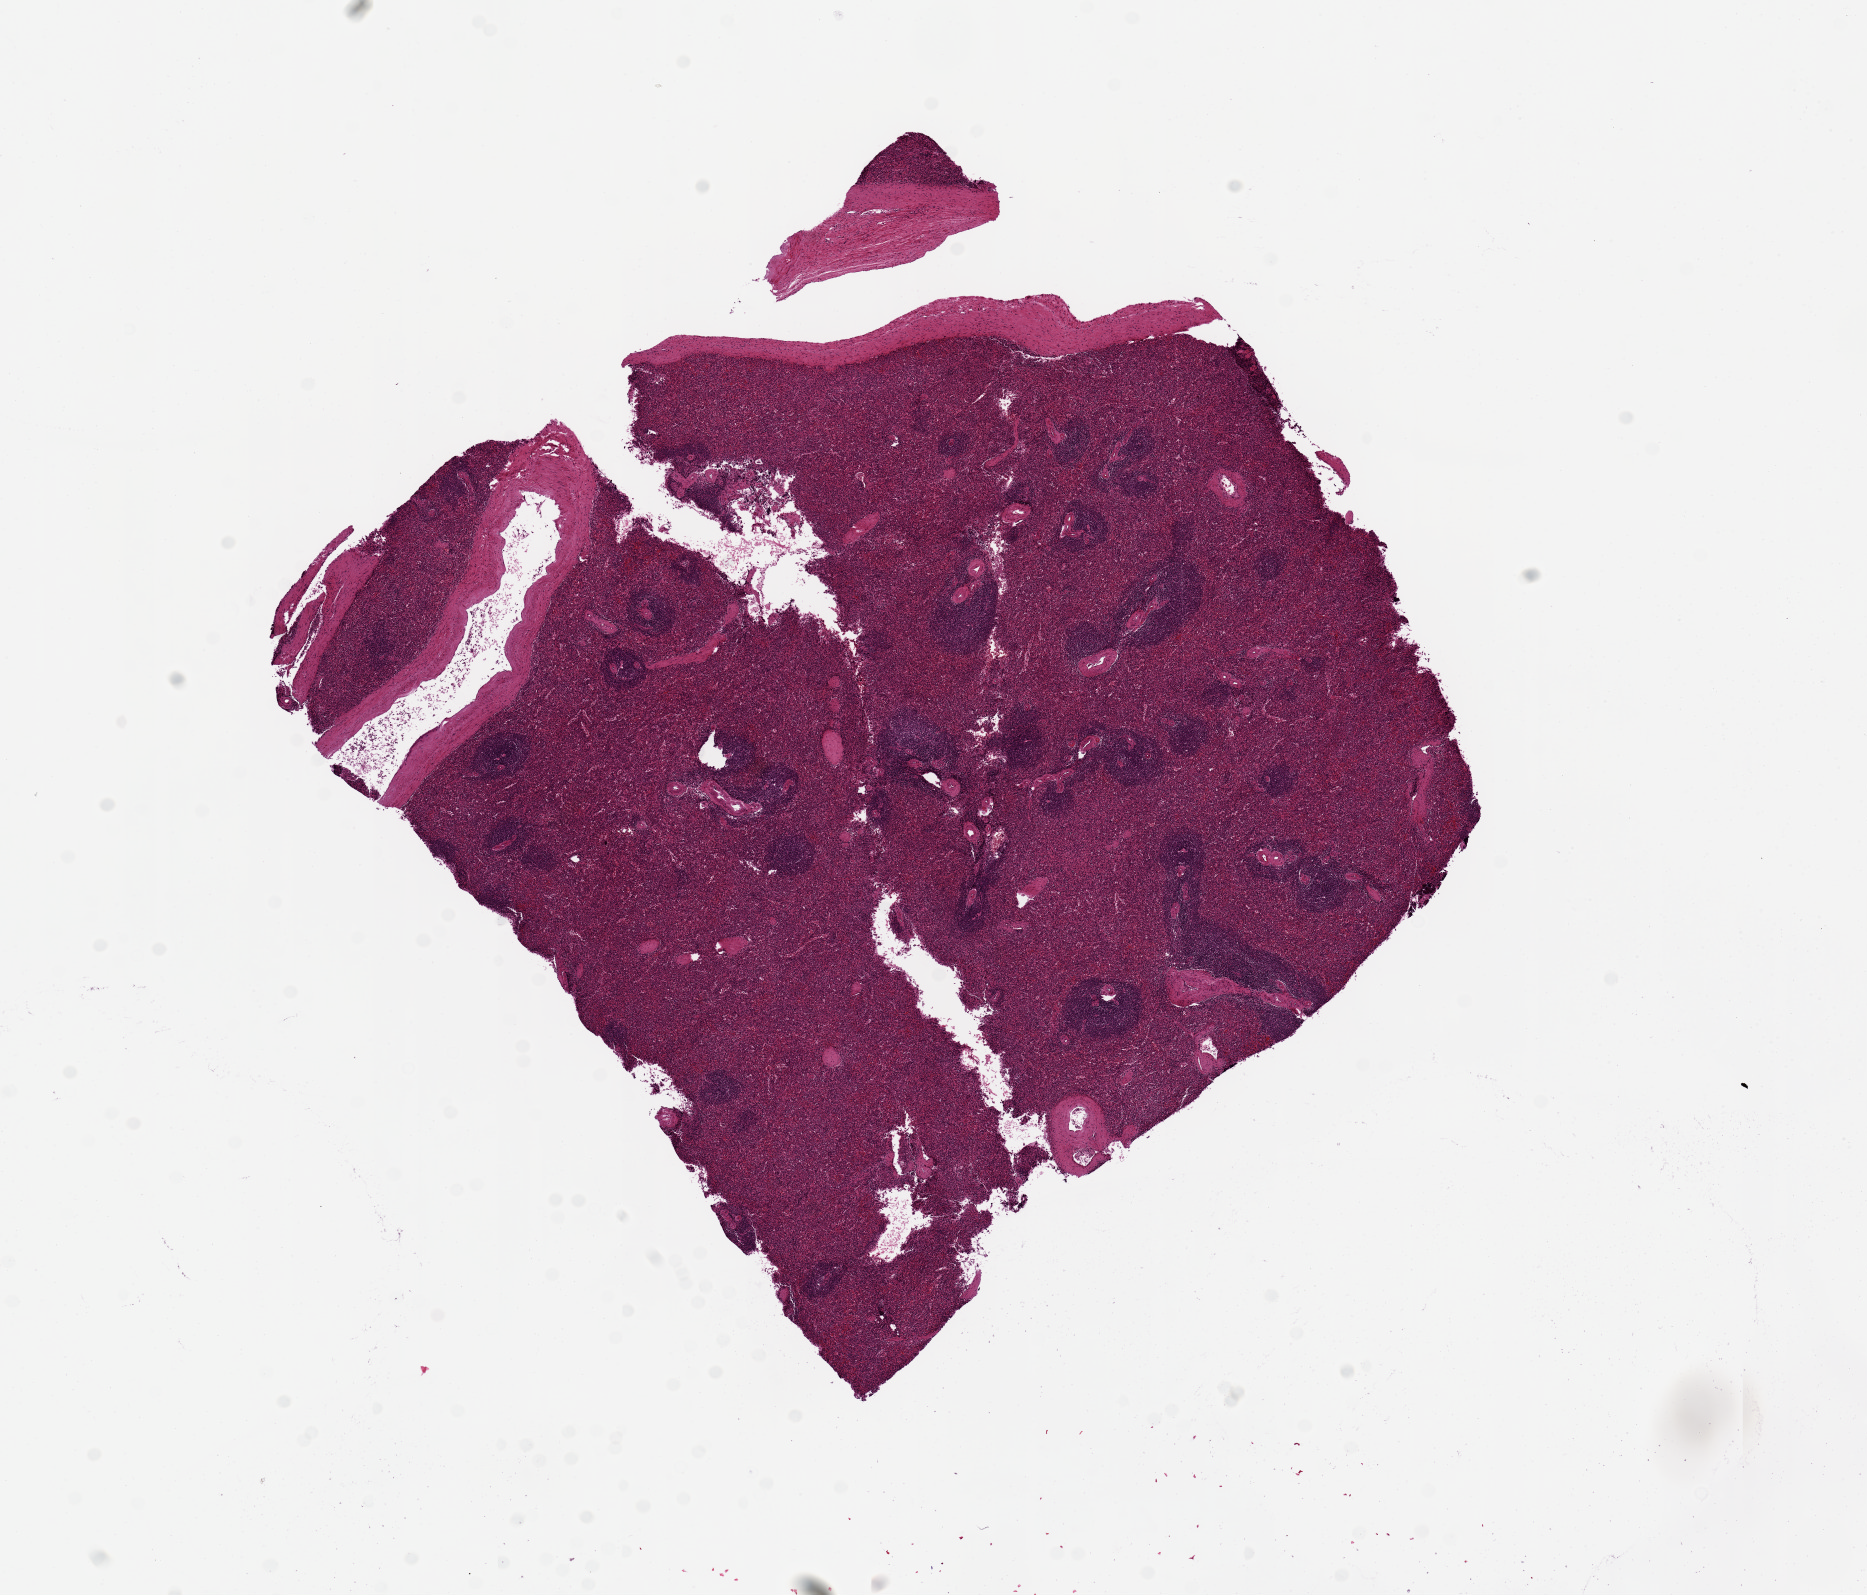
Hematoxylin and eosin (H&E) whole-slide image — shown as a low-resolution overview of the whole scanned area (about 14.8 x 12.6 mm, acquisition: 20x scan). PAXgene-fixed paraffin-embedded (PFPE) section. Section of spleen (target tissue). Donor tissue sample. Male donor.
Reviewer comment on this tissue sample: Moderate congestion and autolysis.